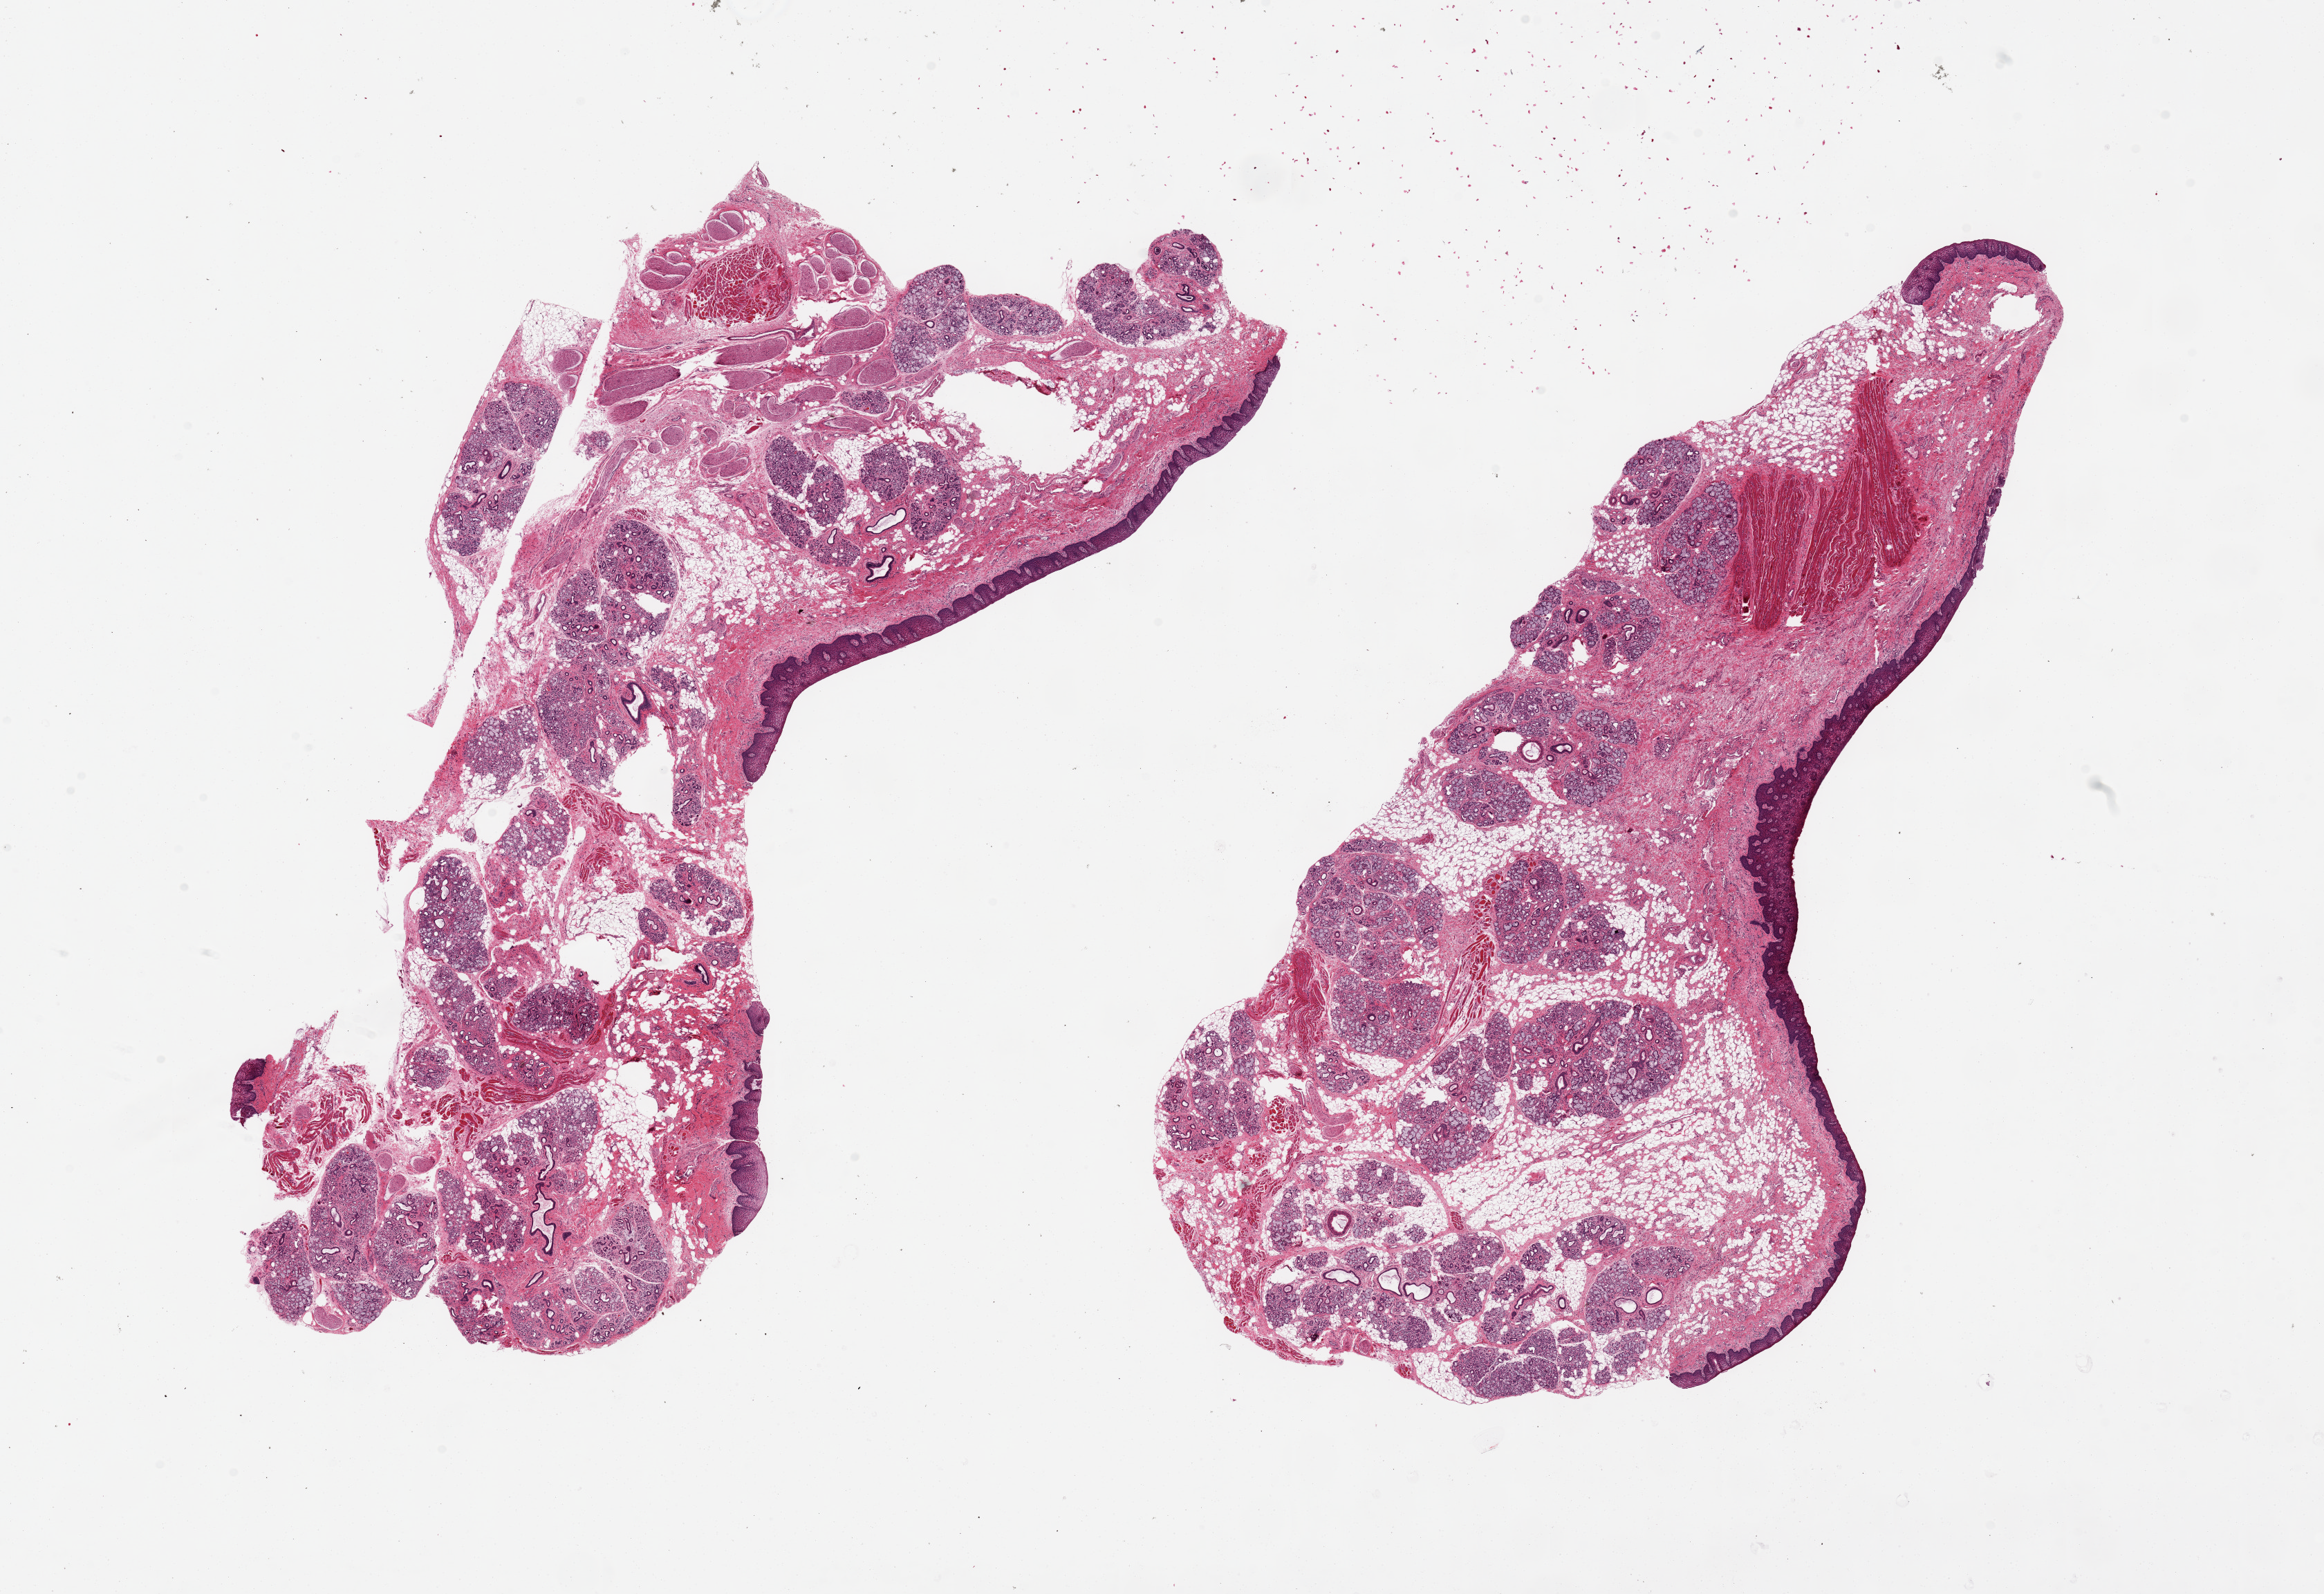
Hematoxylin and eosin (H&E) whole-slide image — low-resolution overview of the scanned area, about 26.6 x 18.2 mm. PAXgene-fixed paraffin-embedded (PFPE) section. Section of minor salivary gland (target tissue). Donor tissue sample. Donor: female.
Pathologist's review note for this sample: 2 pieces, 16x10 & 15x8mm; ~50% glandular elements; rest is mucsoa/stroma.